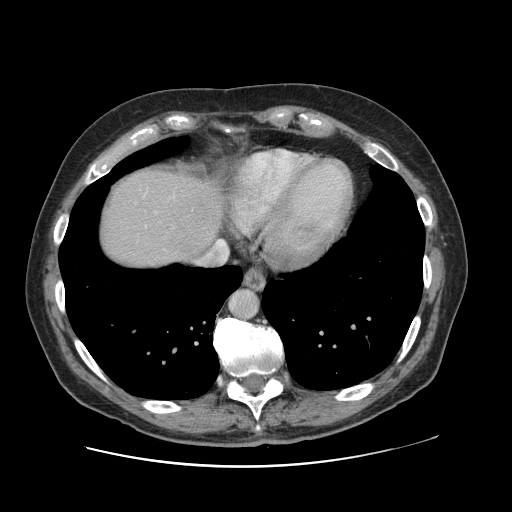
Contrast-enhanced abdominal CT, one axial slice. 120 kVp. Intravenous contrast given. Soft-tissue window (W 400 / L 40 HU). 512 × 512 image matrix, field of view 402 × 402 mm. Male patient, age 71 years. Case-level facts recorded for this patient, not image findings: diagnosis: colorectal cancer liver metastases, imaged before liver resection; multiple liver metastases: no; largest metastasis: 3.3 cm.
Outlined on this slice (manually delineated by an expert):
- hepatic veins: bounding box (x1, y1, x2, y2) in pixels: (197, 240, 228, 266)
- liver: (98, 167, 225, 270)
- planned liver remnant (the part of the liver to remain after resection): (98, 168, 217, 270)